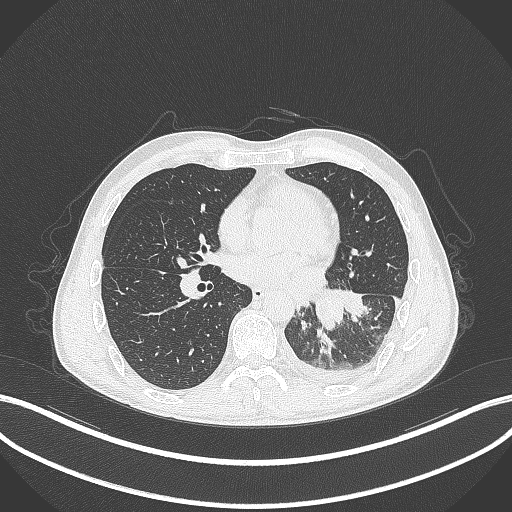
Chest CT, one axial slice; slice 137 of 295 in the series (ordered by position); 120 kVp; lung window (W 1500 / L -600 HU); 512 × 512 image matrix. Male patient, age 47 years. From the clinical record (not read from this slice): clinical TNM (as recorded): T3 N1 M1c; histopathological grade: G3.
Outlined on this slice (rectangle marked by the reading radiologist):
- lung tumour (recorded histology: small cell carcinoma): box from (x=313, y=285) to (x=344, y=334) px